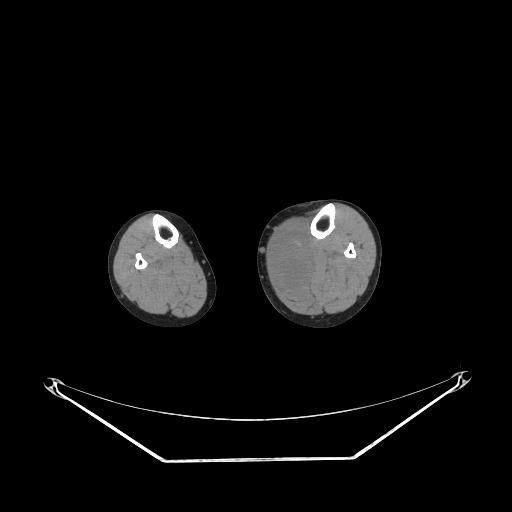
CT of an extremity soft-tissue mass (from a PET/CT study), one axial slice. Slice 134 of 223 in the series (ordered by position). Reconstruction kernel STANDARD. Soft-tissue window (W 400 / L 40 HU). 512 × 512 image matrix, field of view 500 × 500 mm. Female patient. Case-level facts recorded for this patient, not image findings: histological type: extraskeletal high grade osteogenic sarcoma; grade: high; site of the primary tumour: left calf.
Structures marked on this image (expert contour drawn on MRI and transferred to this co-registered scan by the dataset authors):
- gross tumour volume (mass): bounding box <274,233,309,280> (left, top, right, bottom; pixels)